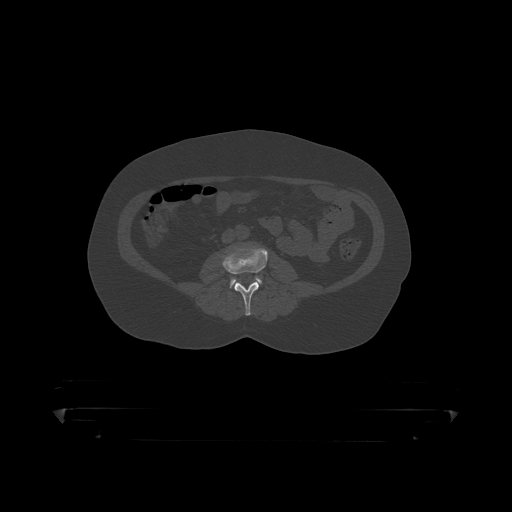
CT including the spine, one axial slice. Slice 83 of 390 in the series (ordered by position). 120 kVp. Bone window (W 1800 / L 400 HU). 1.25 mm slice thickness. 512 × 512 image matrix, field of view 650 × 650 mm. Male patient, age 60 years. Case-level facts recorded for this patient, not image findings: primary cancer: prostate.
Structures marked on this image (semi-automatically segmented with operator editing):
- L3 vertebra: bounding box [x1, y1, x2, y2] px = [222, 245, 268, 316]
- L4 vertebra: [231, 277, 262, 286]